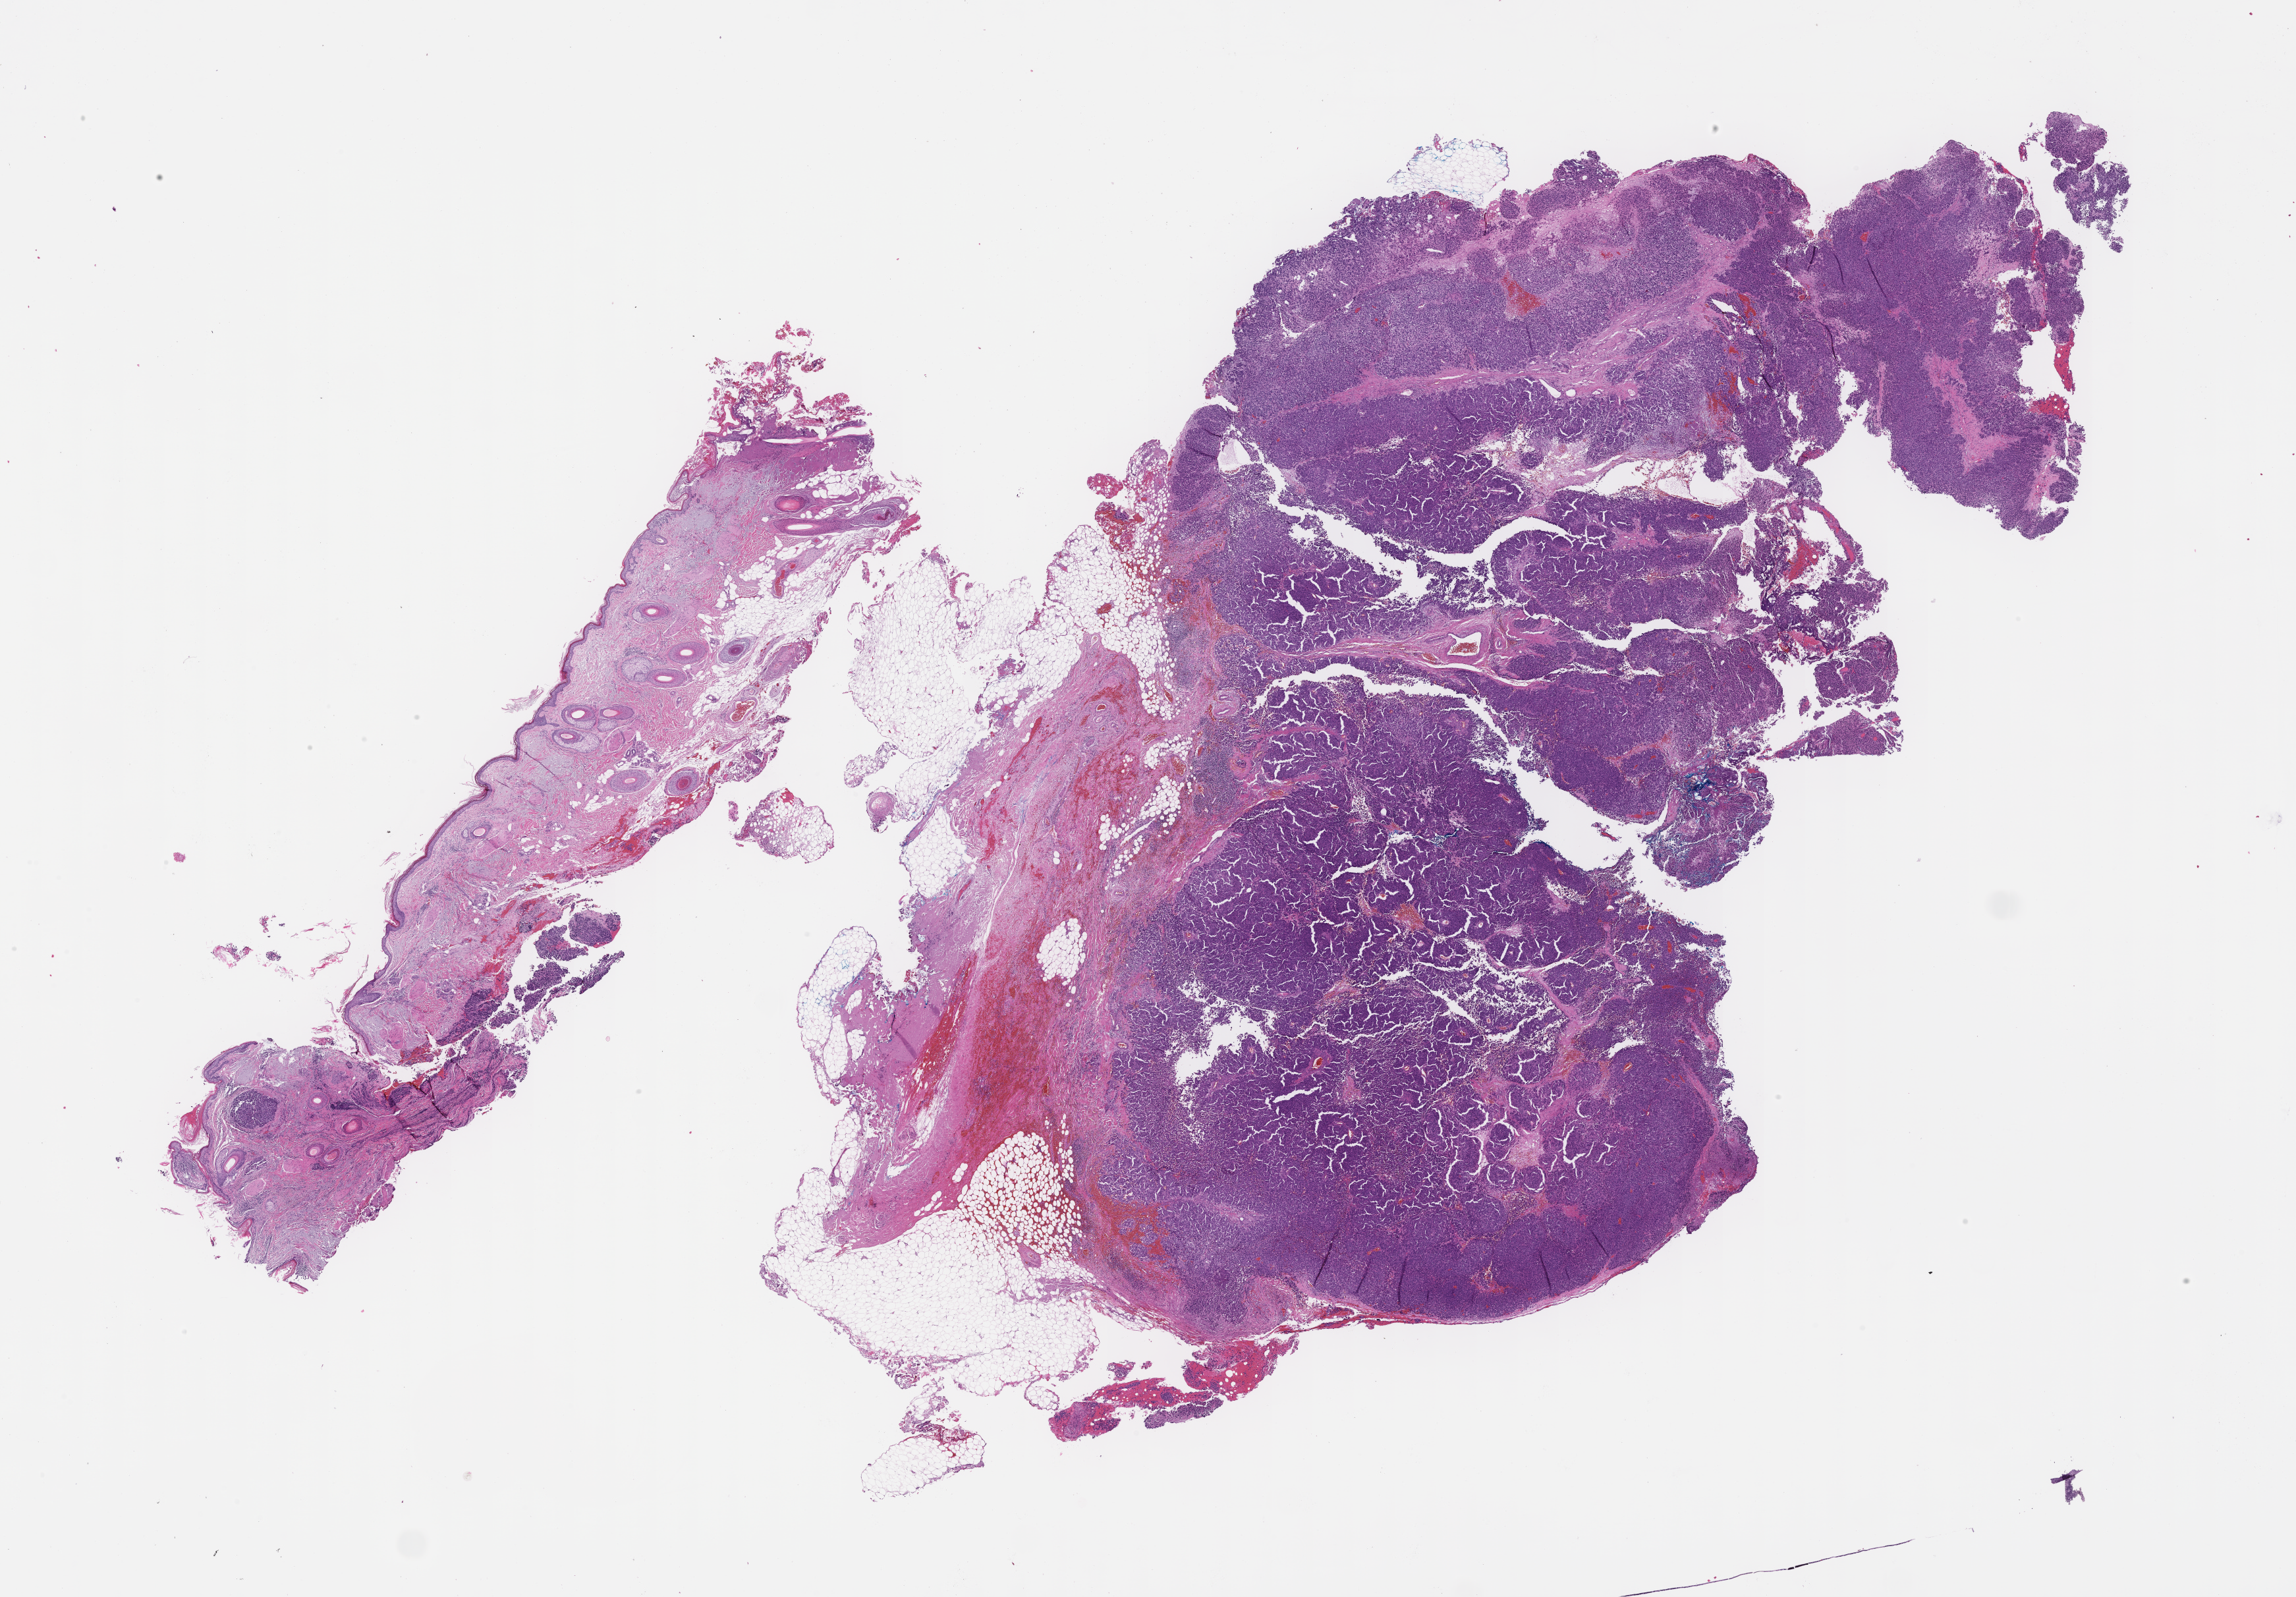
Hematoxylin and eosin (H&E) whole-slide image — low-resolution overview of the scanned area, about 28.1 x 19.6 mm, formalin-fixed paraffin-embedded section. Patient sex: female.
This section: metastasis (sampled organ not recorded). Primary diagnosis of the patient: Melanoma.